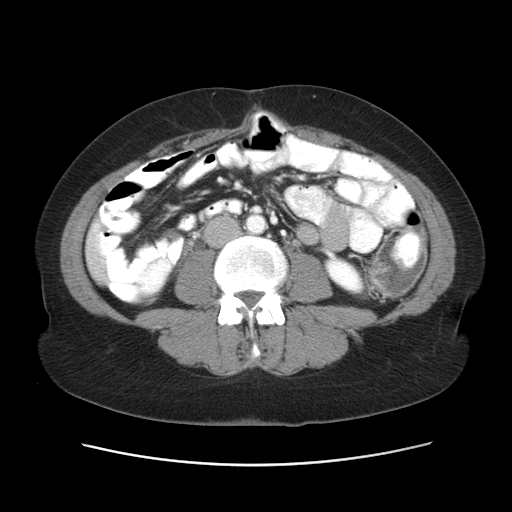
Contrast-enhanced abdominal CT, one axial slice; slice 12 of 52 in the series (ordered by position); reconstruction kernel STANDARD; 120 kVp; intravenous contrast given; soft-tissue window (W 400 / L 40 HU); 512 × 512 image matrix. Female patient, age 48 years. From the clinical record (not read from this slice): diagnosis: colorectal cancer liver metastases, imaged before liver resection; multiple liver metastases: yes; largest metastasis: 4.5 cm; disease in both lobes: yes.
Outlined on this slice (expert manual segmentation):
- liver: bounding box <93,255,104,273> (left, top, right, bottom; pixels)